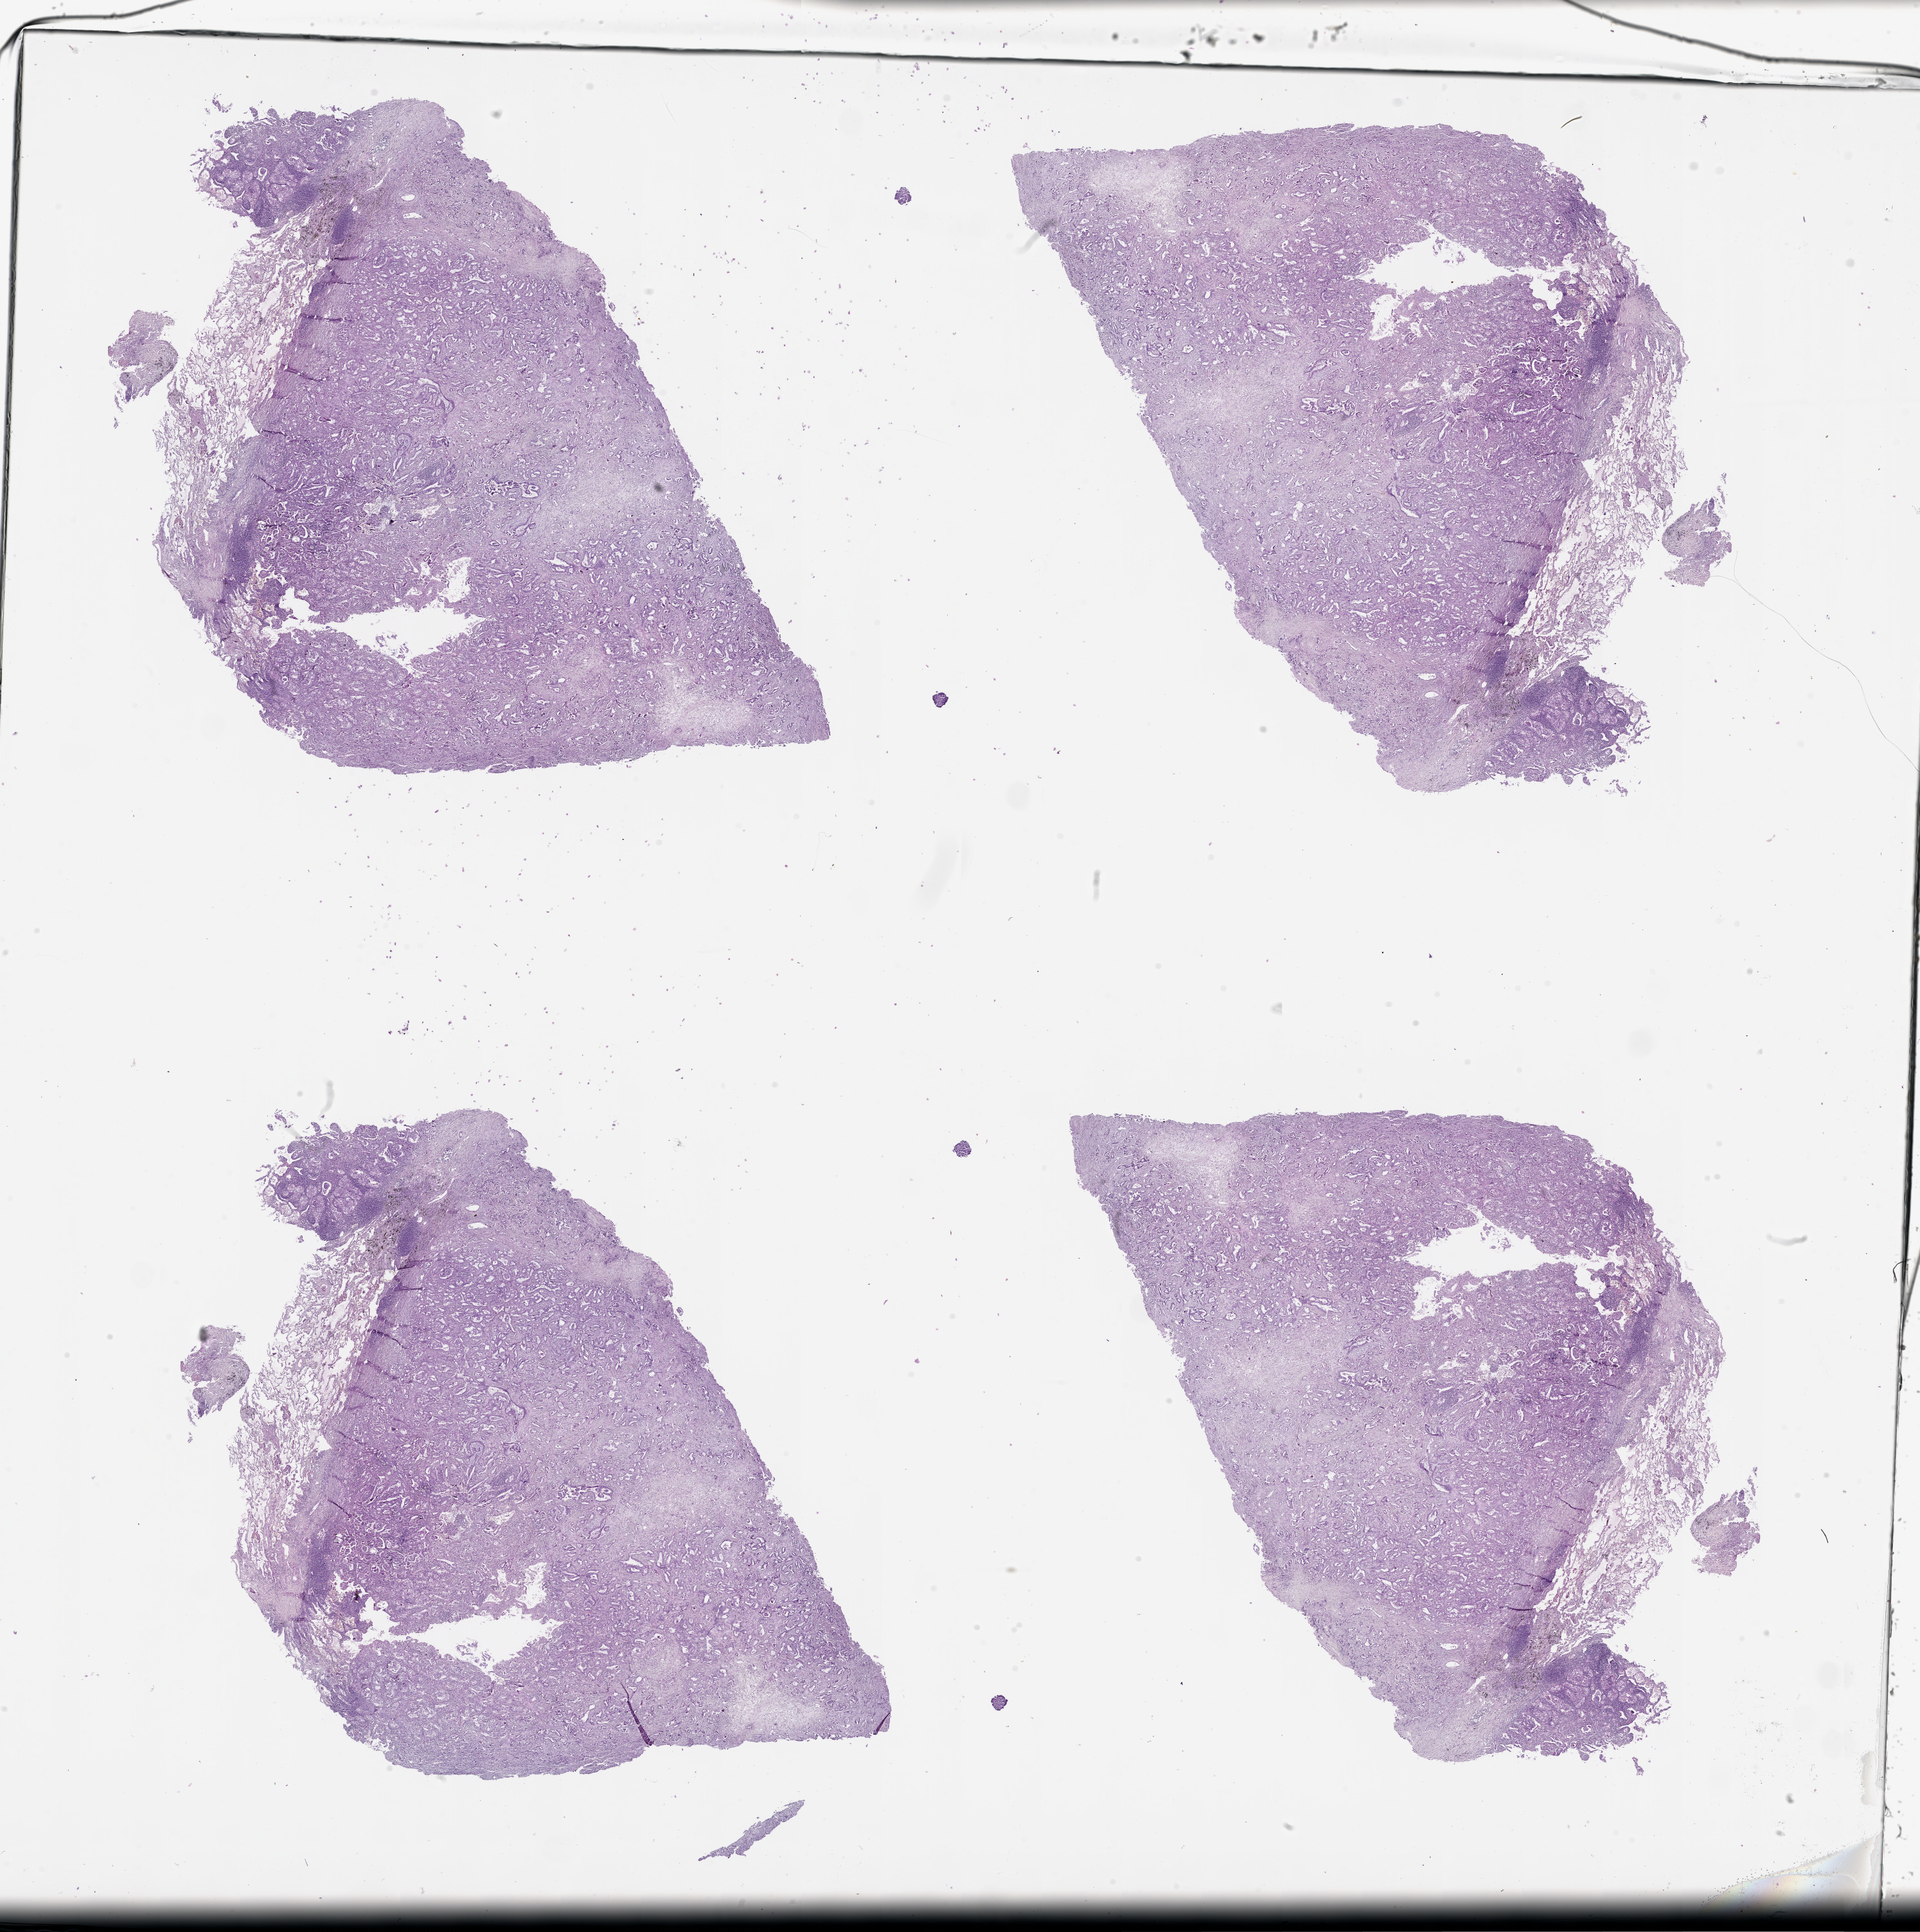
Digitized H&E tissue section (whole slide), whole scanned area (about 24.1 x 24.2 mm, slide scanned at 20x) shown as a low-resolution overview. Tumour tissue sample, lung. Patient: male, age 61 years. Histologic grade: G2 (moderately differentiated).
Primary tumour site (as recorded): right upper lobe. Histologic diagnosis: Adenocarcinoma, NOS. AJCC pathologic stage: IIIA.